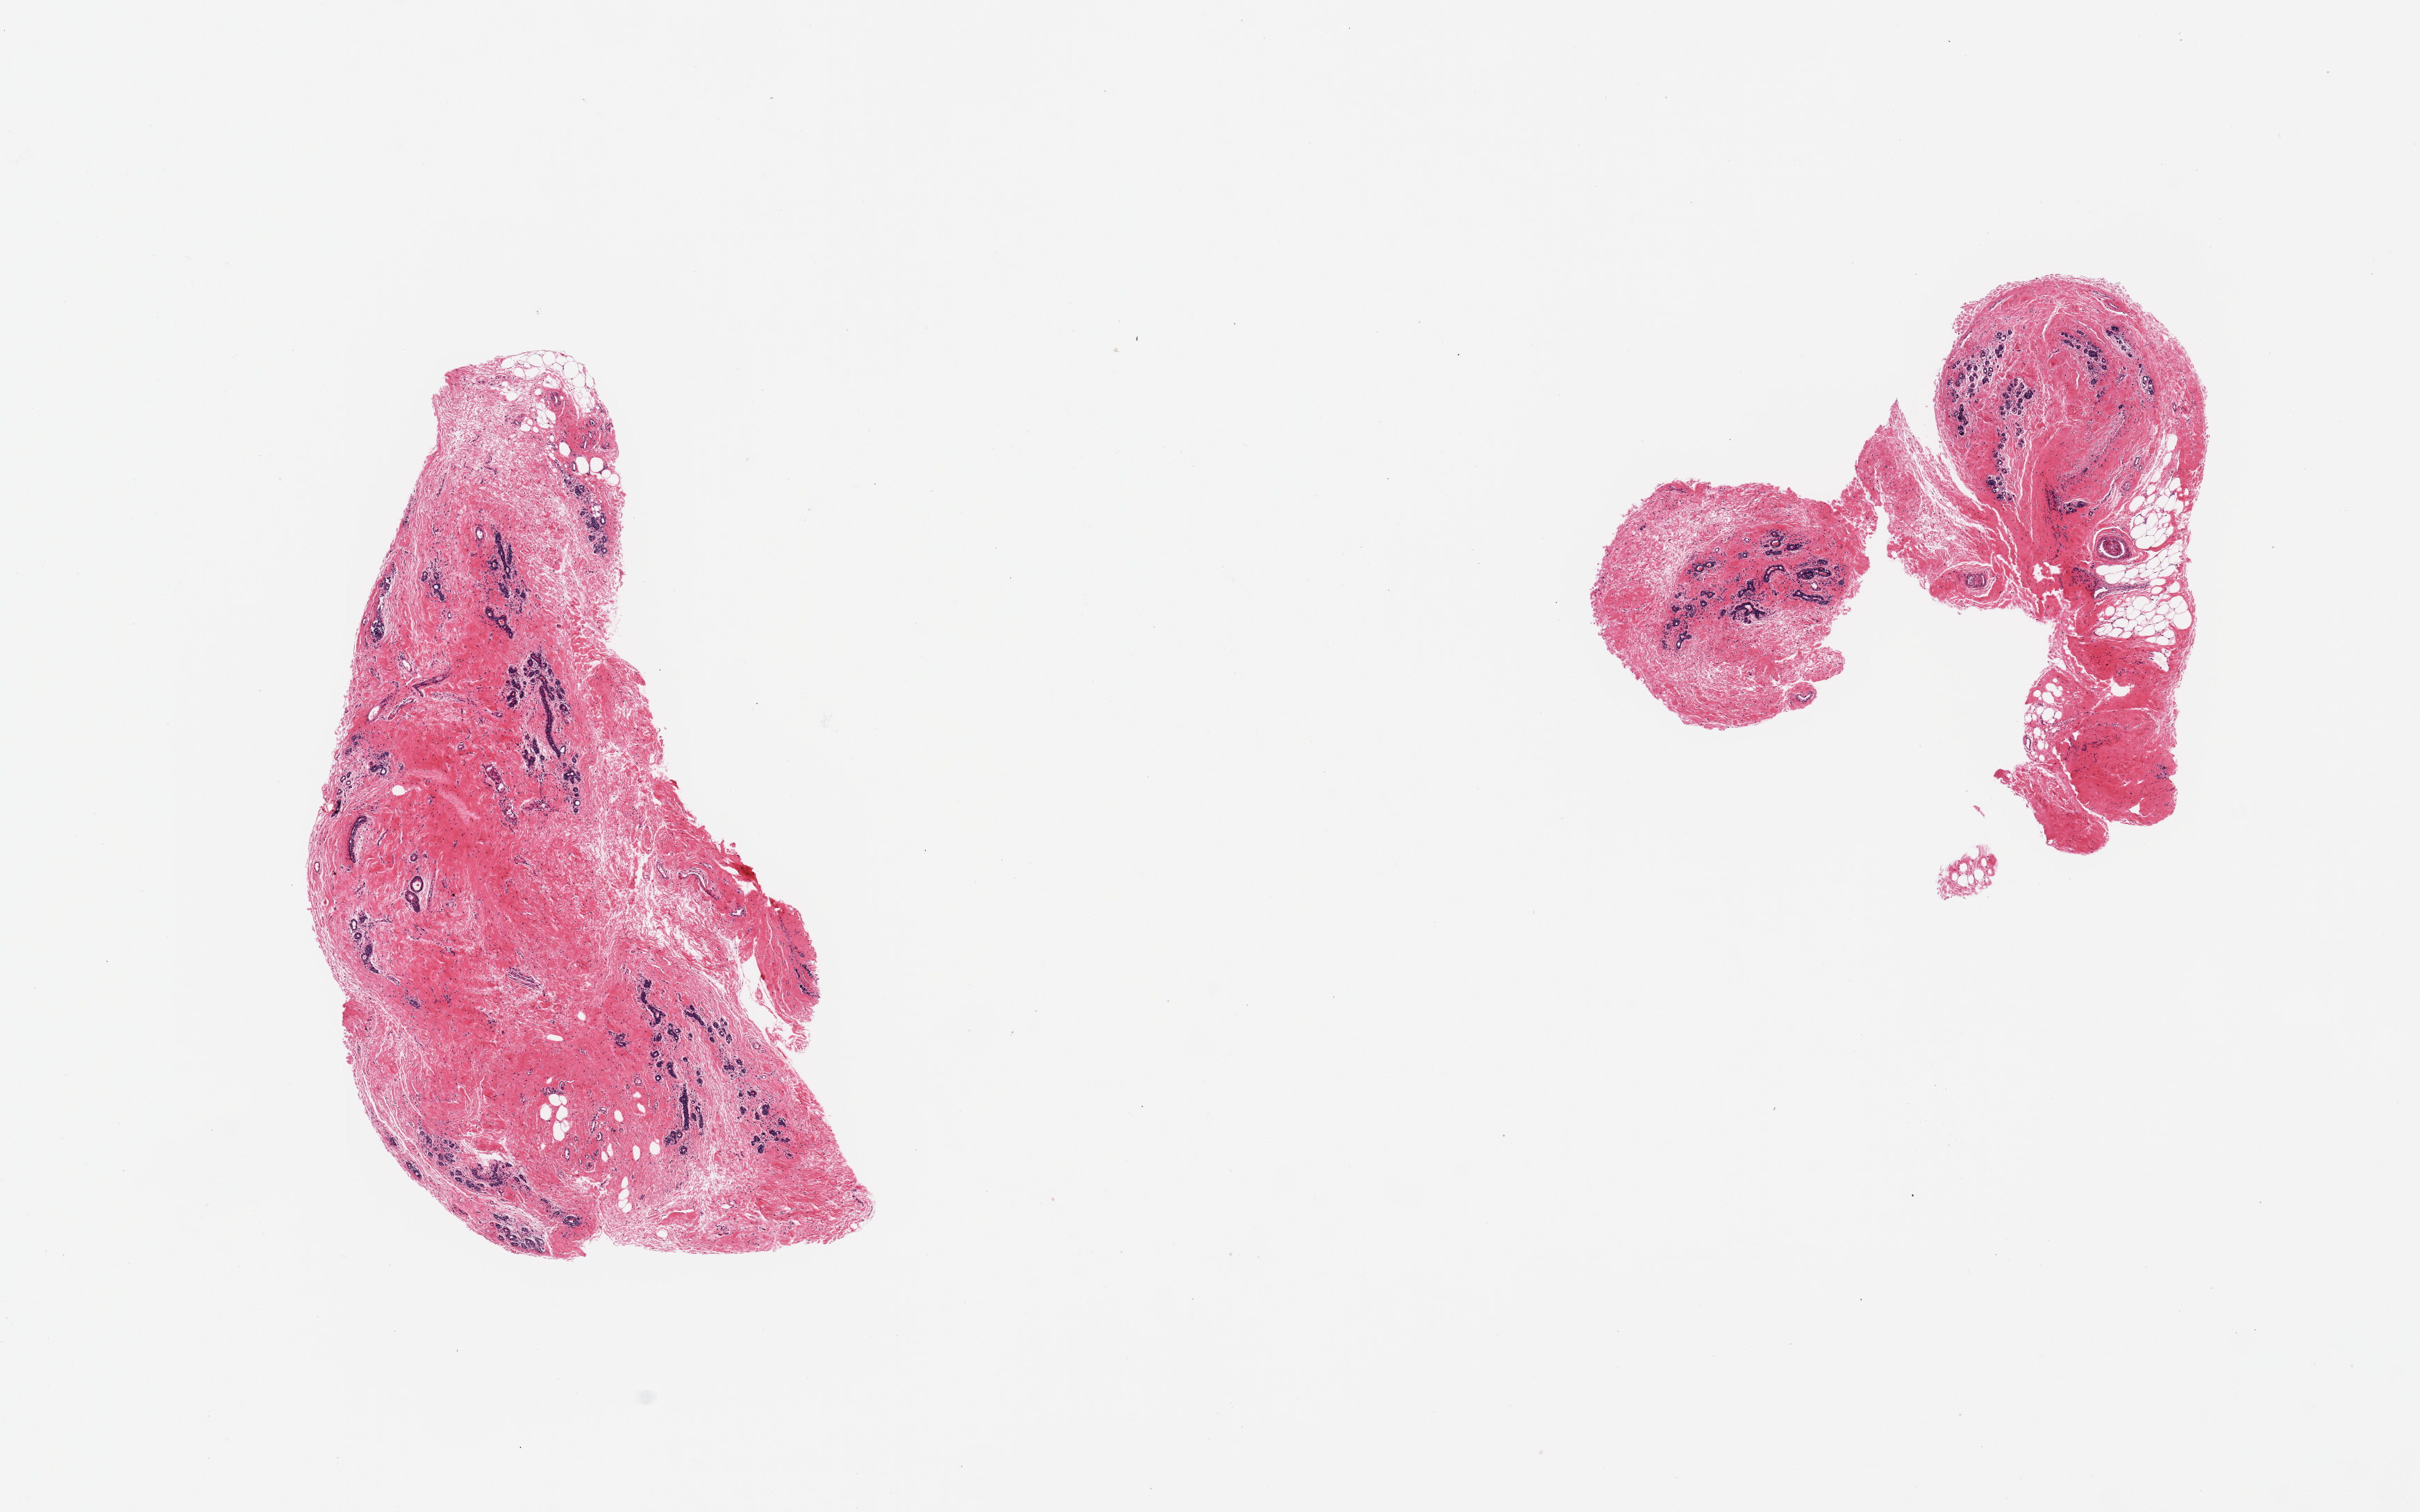
Digitized haematoxylin and eosin-stained section — a low-resolution overview of the entire scanned area, about 13.8 x 8.6 mm (slide scanned at 20x). PAXgene-fixed, paraffin-embedded tissue. Target tissue: breast. Donor tissue sample. Donor sex: female.
Reviewer comment on this tissue sample: 2 pieces, mammary ductal/lobular elements present, inactive/atrophic for stated age.